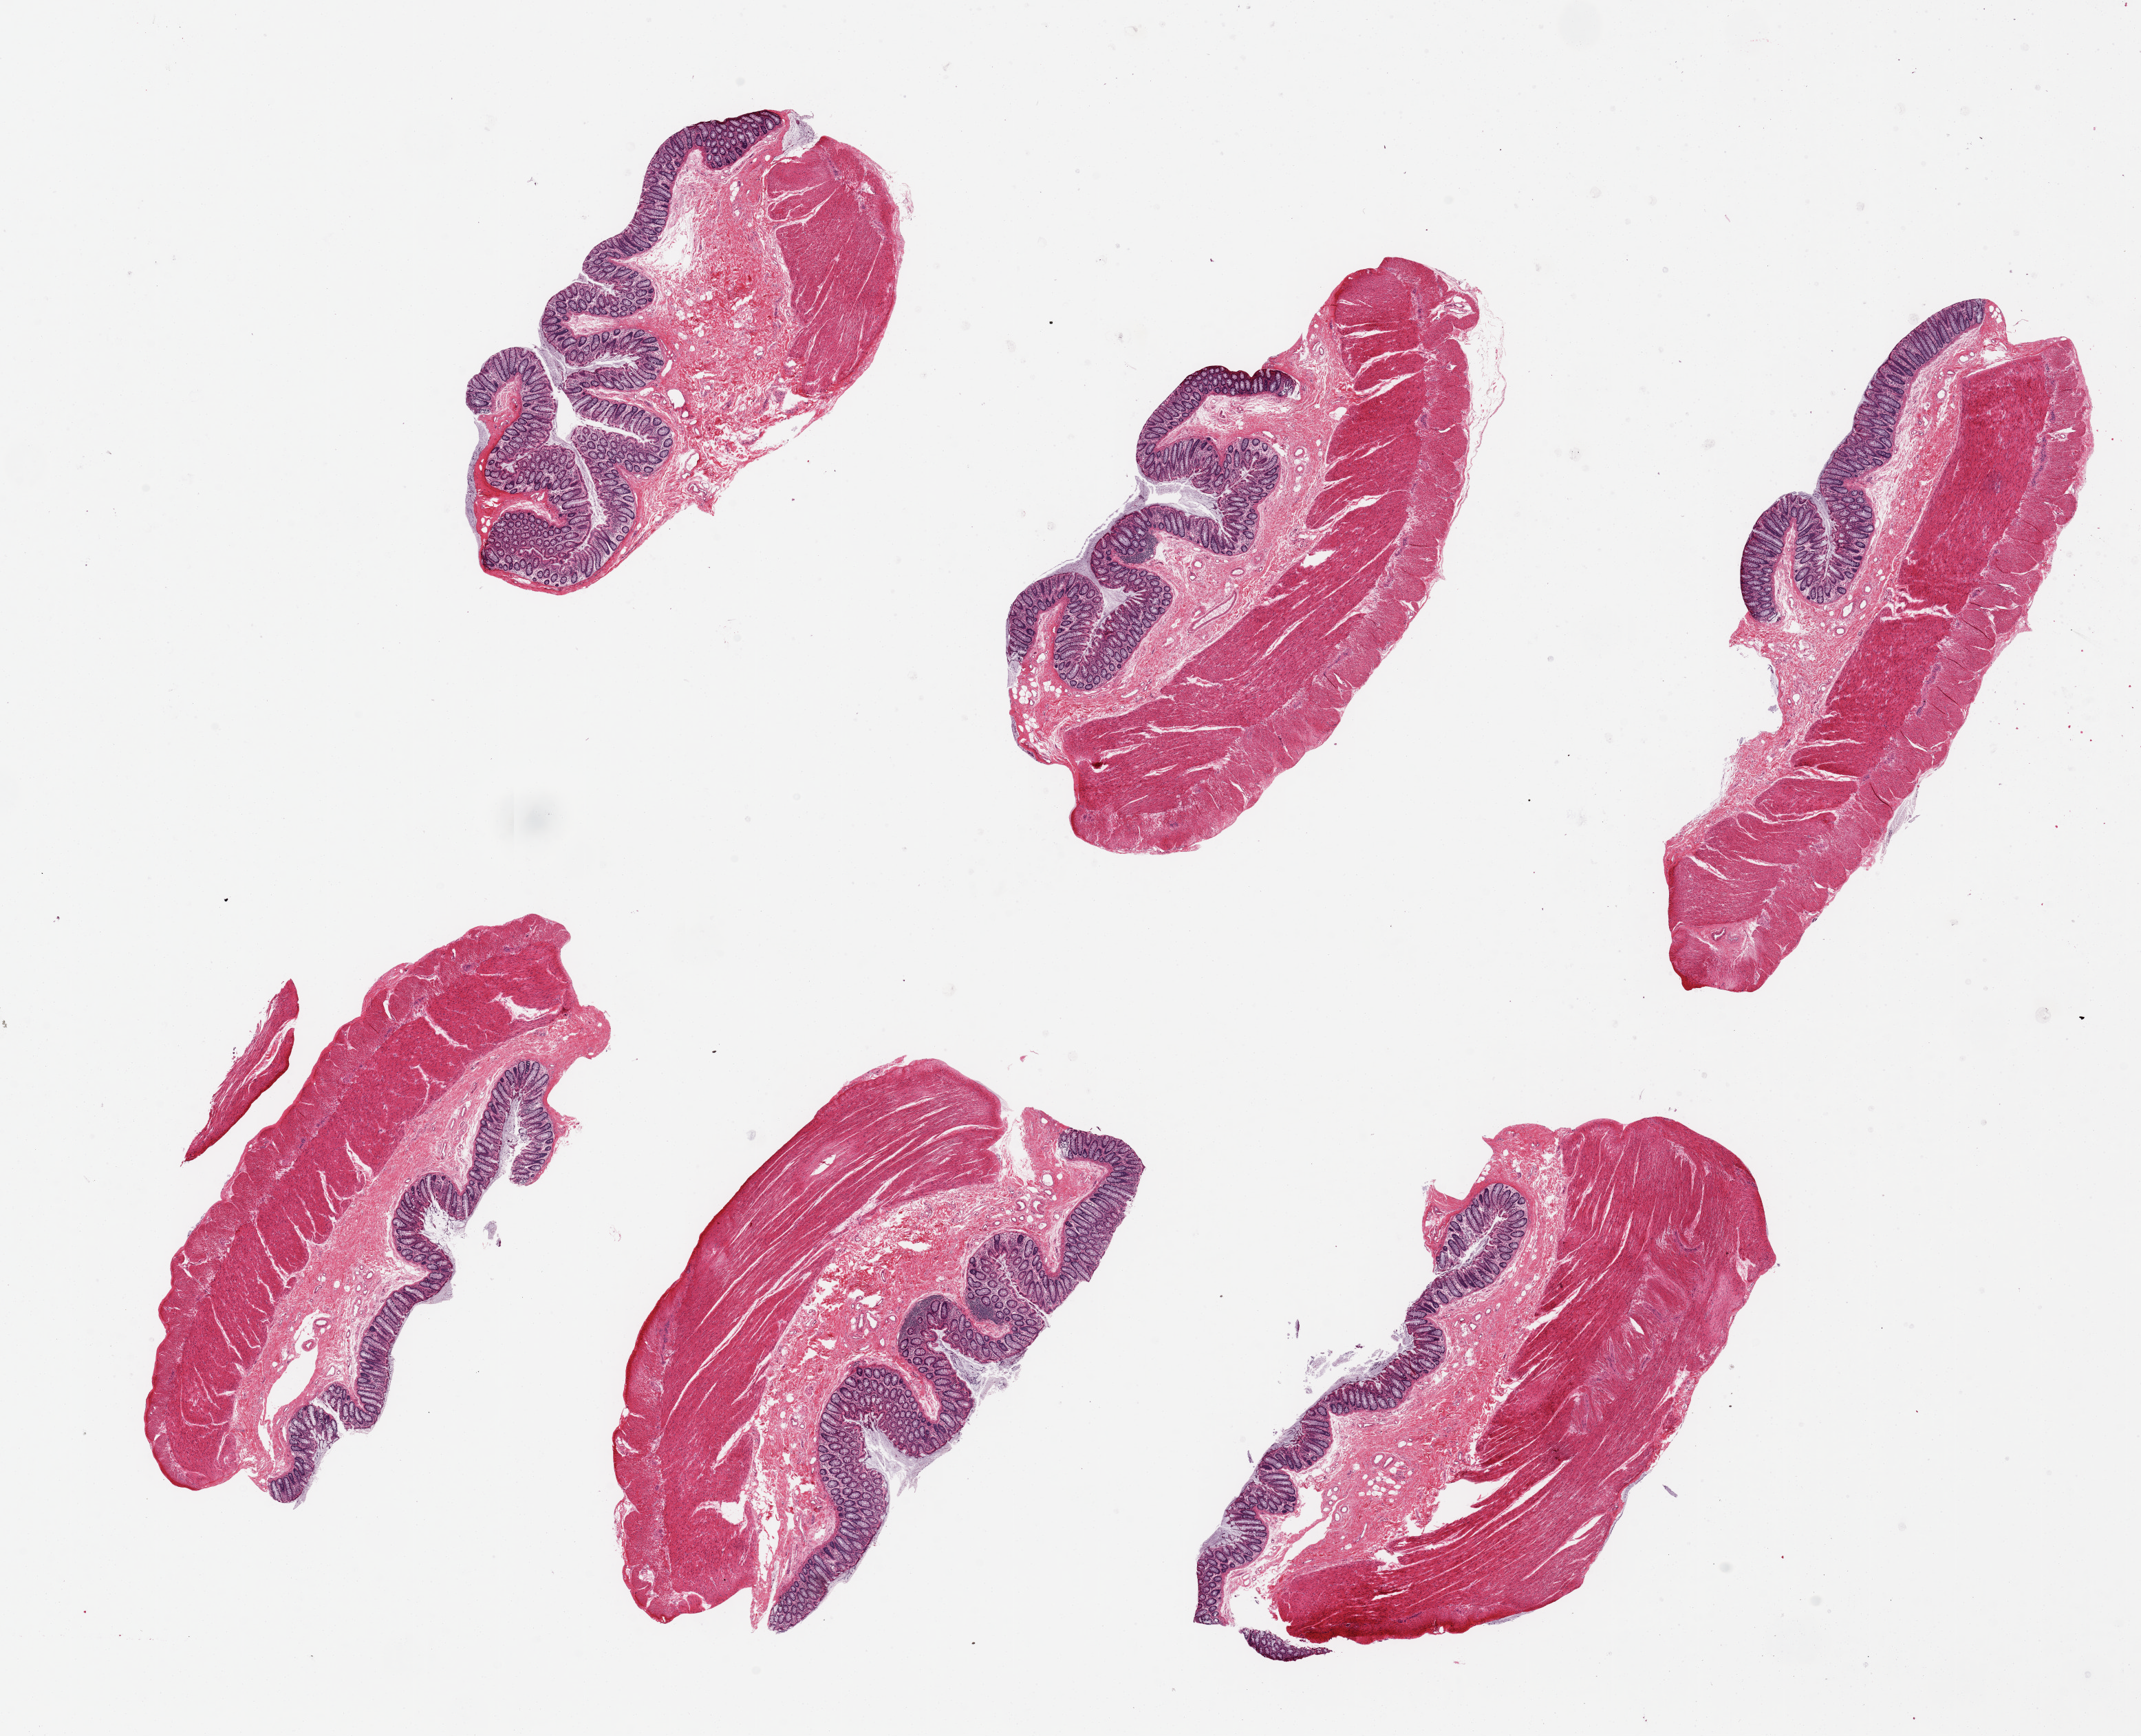
Haematoxylin and eosin whole-slide image, low-resolution overview of the scanned area, about 24.6 x 20.0 mm (from a 20x scan), PAXgene-fixed, paraffin-embedded tissue, target tissue: transverse colon, tissue donor sample. Donor: female.
Reviewer comment on this tissue sample: 6 pieces up to 8x3 mm; good mucosal preservation.